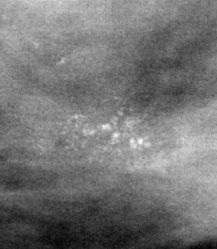
Cropped region of a digitized screen-film mammogram centred on a radiologist-marked abnormality, right breast, MLO view.
- Calcifications, morphology pleomorphic, distribution clustered; BI-RADS assessment category 4; subtlety rating 3 on a 1 (subtle) to 5 (obvious) scale; pathology (as recorded): benign.